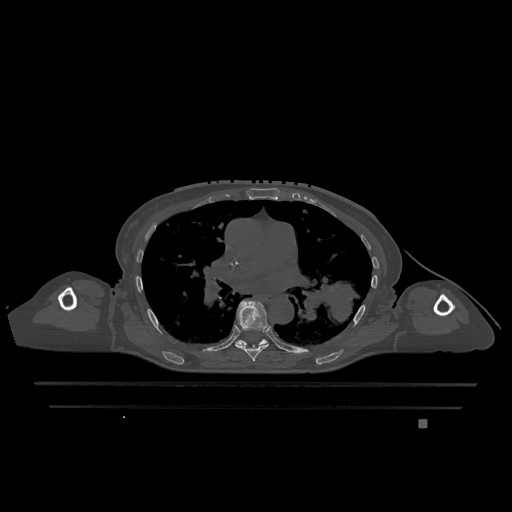
CT including the spine, one axial slice; slice 771 of 1317 in the series (ordered by position); bone window (W 1800 / L 400 HU); 0.5 mm slice thickness; 512 × 512 image matrix, field of view 500 × 500 mm. Female patient, age 74 years. Case-level facts recorded for this patient, not image findings: primary cancer: lung; vertebrae with lytic lesions (as recorded): T1, T4, T5, T6, L4, L5.
Outlined on this slice (semi-automatic segmentation, software-assisted and operator-edited):
- T6 vertebra: bounding box [x1, y1, x2, y2] px = [235, 300, 270, 361]
- T7 vertebra: [235, 339, 268, 346]